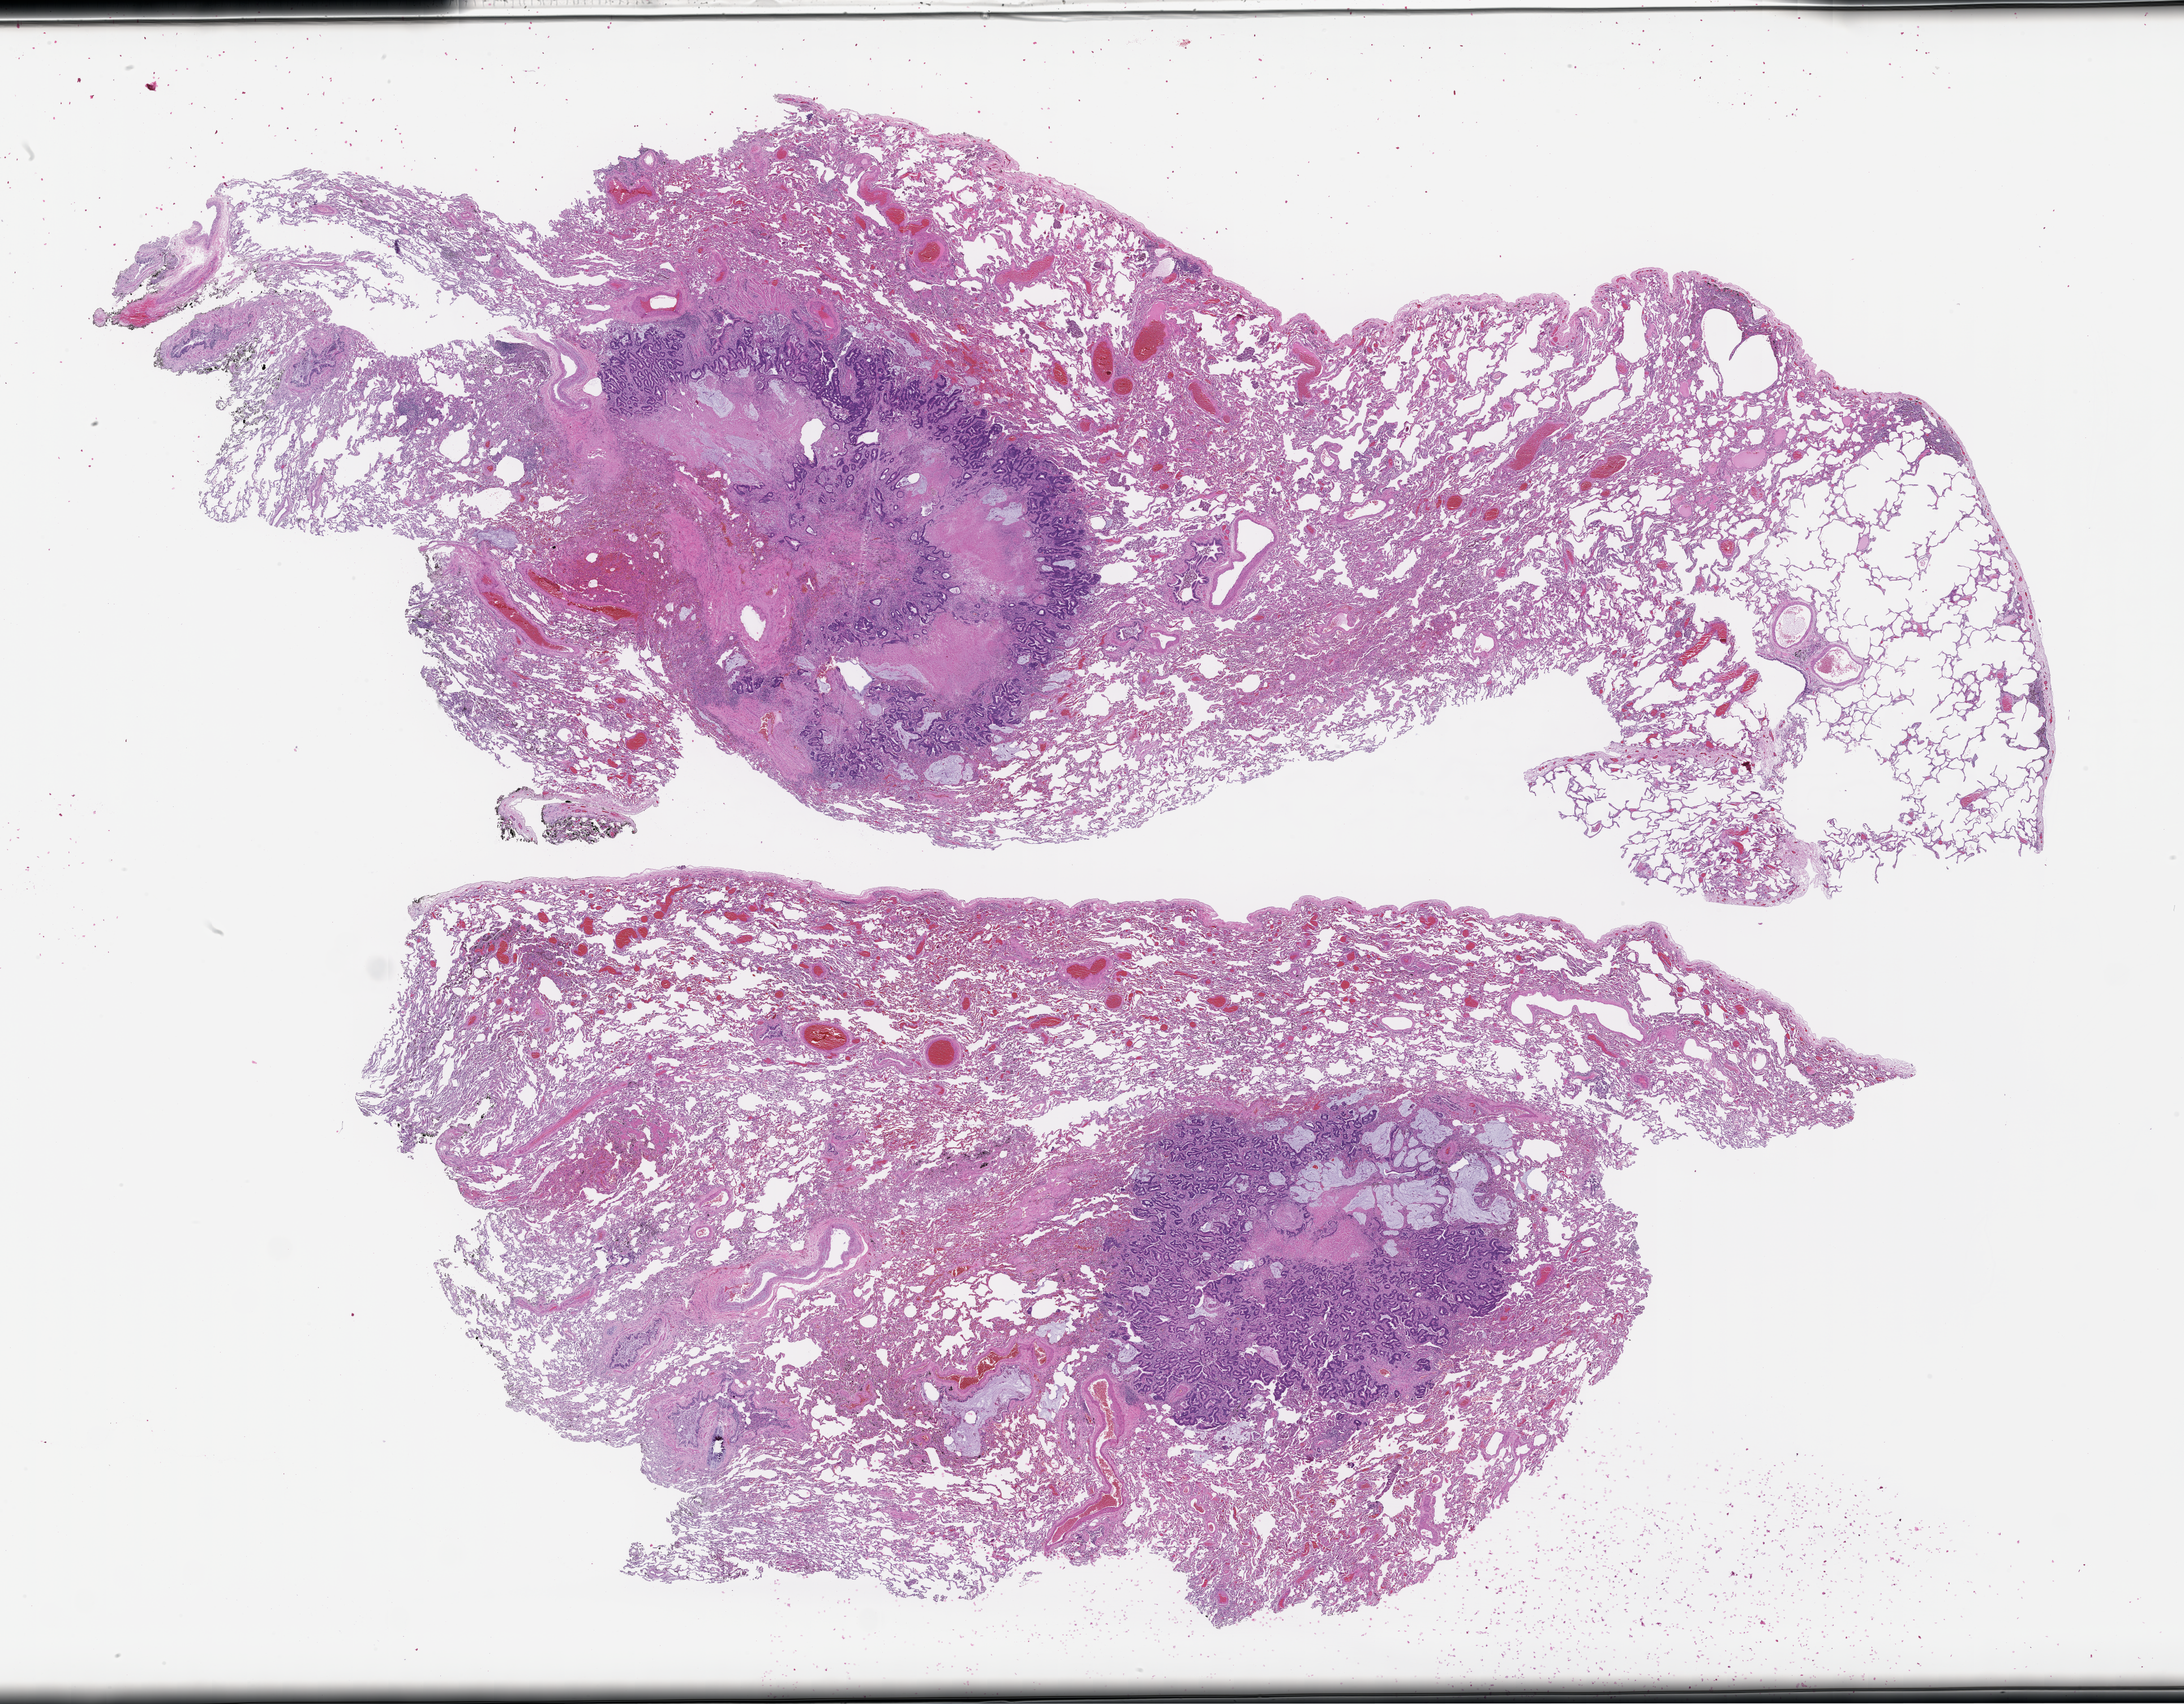
Digitized H&E-stained section — whole scanned area (about 31.2 x 24.3 mm) shown as a low-resolution overview; FFPE section; specimen time point: archival tissue. Female patient.
• this section: metastasis (sampled organ not recorded)
• primary diagnosis of the patient: Colorectal Carcinoma